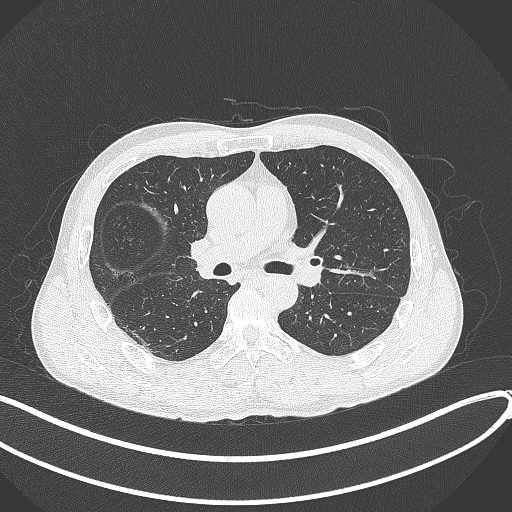
Chest CT, one axial slice. Position 225 of 409 along the scan axis. Reconstruction kernel B70f. 120 kVp. Lung window (W 1500 / L -600 HU). 1 mm slice thickness. 512 × 512 image matrix, field of view 400 × 400 mm. Male patient, age 53 years. Case-level facts recorded for this patient, not image findings: clinical TNM (as recorded): T1b N0 M0.
Annotated regions visible in this slice (rectangle marked by the reading radiologist):
- lung tumour (recorded histology: squamous cell carcinoma): bounding box (x1, y1, x2, y2) in pixels: (187, 232, 224, 285)